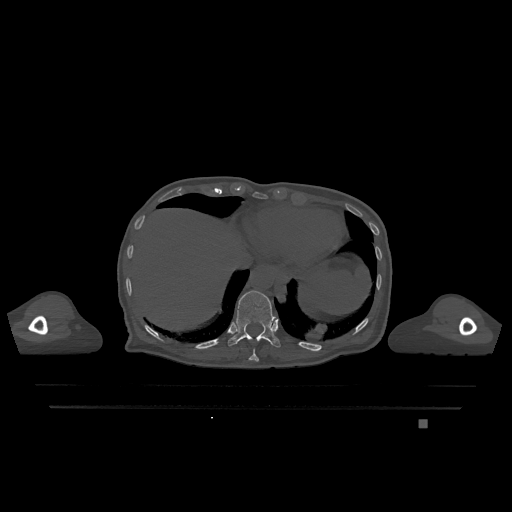
CT including the spine, one axial slice; position 601 of 1317 along the scan axis; bone window (W 1800 / L 400 HU); 0.5 mm slice thickness; 512 × 512 image matrix, field of view 500 × 500 mm. Patient: female, 74 years. From the clinical record (not read from this slice): primary cancer: lung.
Outlined on this slice (semi-automatic segmentation, software-assisted and operator-edited):
- T10 vertebra: bounding box [x1, y1, x2, y2] px = [249, 349, 259, 362]
- T11 vertebra: [228, 290, 281, 348]